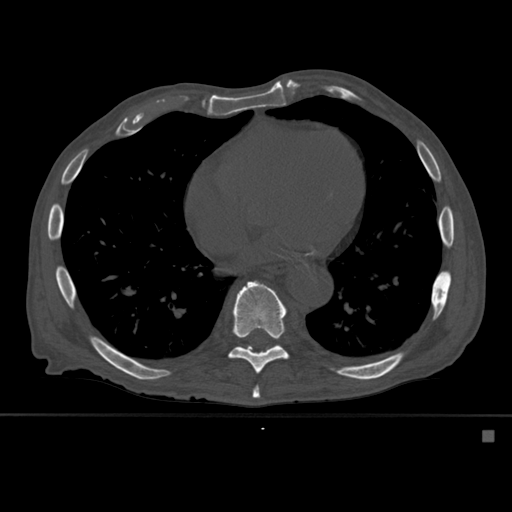
CT including the spine, one axial slice; position 333 of 527 along the scan axis; bone window (W 1800 / L 400 HU); 512 × 512 image matrix. Patient: male, 78 years. Case-level facts recorded for this patient, not image findings: primary cancer: prostate.
Annotated regions visible in this slice (semi-automatically segmented with operator editing):
- T8 vertebra: bounding box (x1, y1, x2, y2) in pixels: (252, 386, 260, 399)
- T9 vertebra: (228, 281, 289, 376)